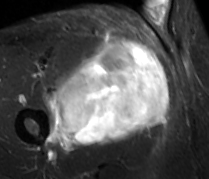
MRI of an extremity soft-tissue mass, one axial slice; position 48 of 89 along the scan axis; STIR; MR volume resampled by the dataset authors to the PET/CT grid (not the native acquisition matrix); 3.27 mm slice thickness; 209 × 179 image matrix, field of view 204 × 175 mm. Male patient. Case-level facts recorded for this patient, not image findings: histological type: undifferentiated - pleiomorphic; grade: high; site of the primary tumour: right thigh.
Outlined on this slice (expert contour drawn on MRI and transferred to this co-registered scan by the dataset authors):
- gross tumour volume including surrounding oedema: box from (x=44, y=36) to (x=170, y=150) px
- gross tumour volume (mass): (x=55, y=39)–(x=170, y=145)